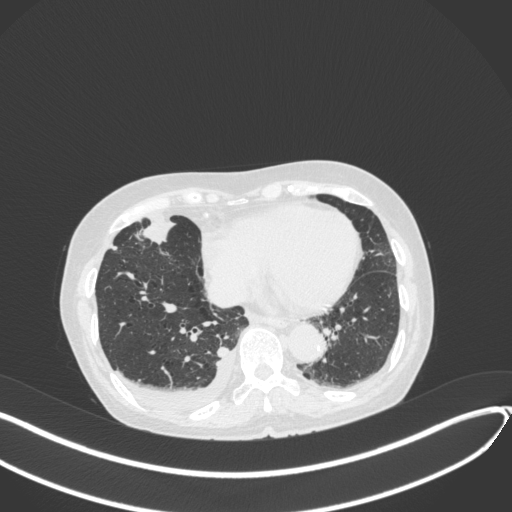
Chest CT, one axial slice. Position 122 of 418 along the scan axis. Reconstruction kernel B31f. Lung window (W 1500 / L -600 HU). 1 mm slice thickness. 512 × 512 image matrix, field of view 400 × 400 mm. Patient: female, 75 years. Case-level facts recorded for this patient, not image findings: clinical TNM (as recorded): T2a N3 M0.
Outlined on this slice (rectangle marked by the reading radiologist):
- lung tumour (recorded histology: adenocarcinoma): box from (x=136, y=211) to (x=180, y=250) px